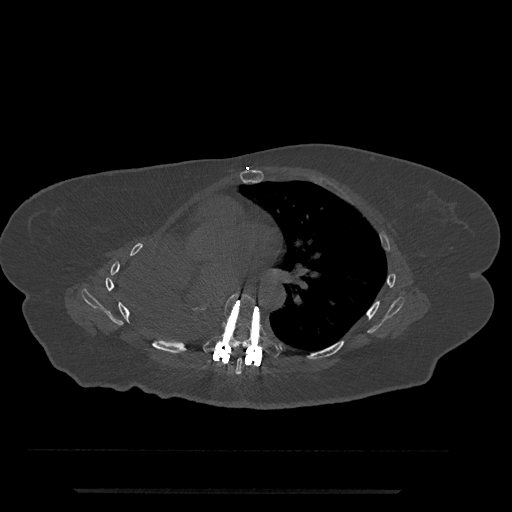
CT including the spine, one axial slice; position 455 of 797 along the scan axis; reconstruction kernel Br40s/3; bone window (W 1800 / L 400 HU); 0.5 mm slice thickness; 512 × 512 image matrix, field of view 440 × 440 mm. Female patient, age 51 years. Case-level facts recorded for this patient, not image findings: primary cancer: neuro; vertebrae with lytic lesions (as recorded): T8.
Annotated regions visible in this slice (semi-automatically segmented with operator editing):
- T6 vertebra: bounding box [x1, y1, x2, y2] px = [235, 358, 242, 375]
- T7 vertebra: [203, 293, 281, 358]